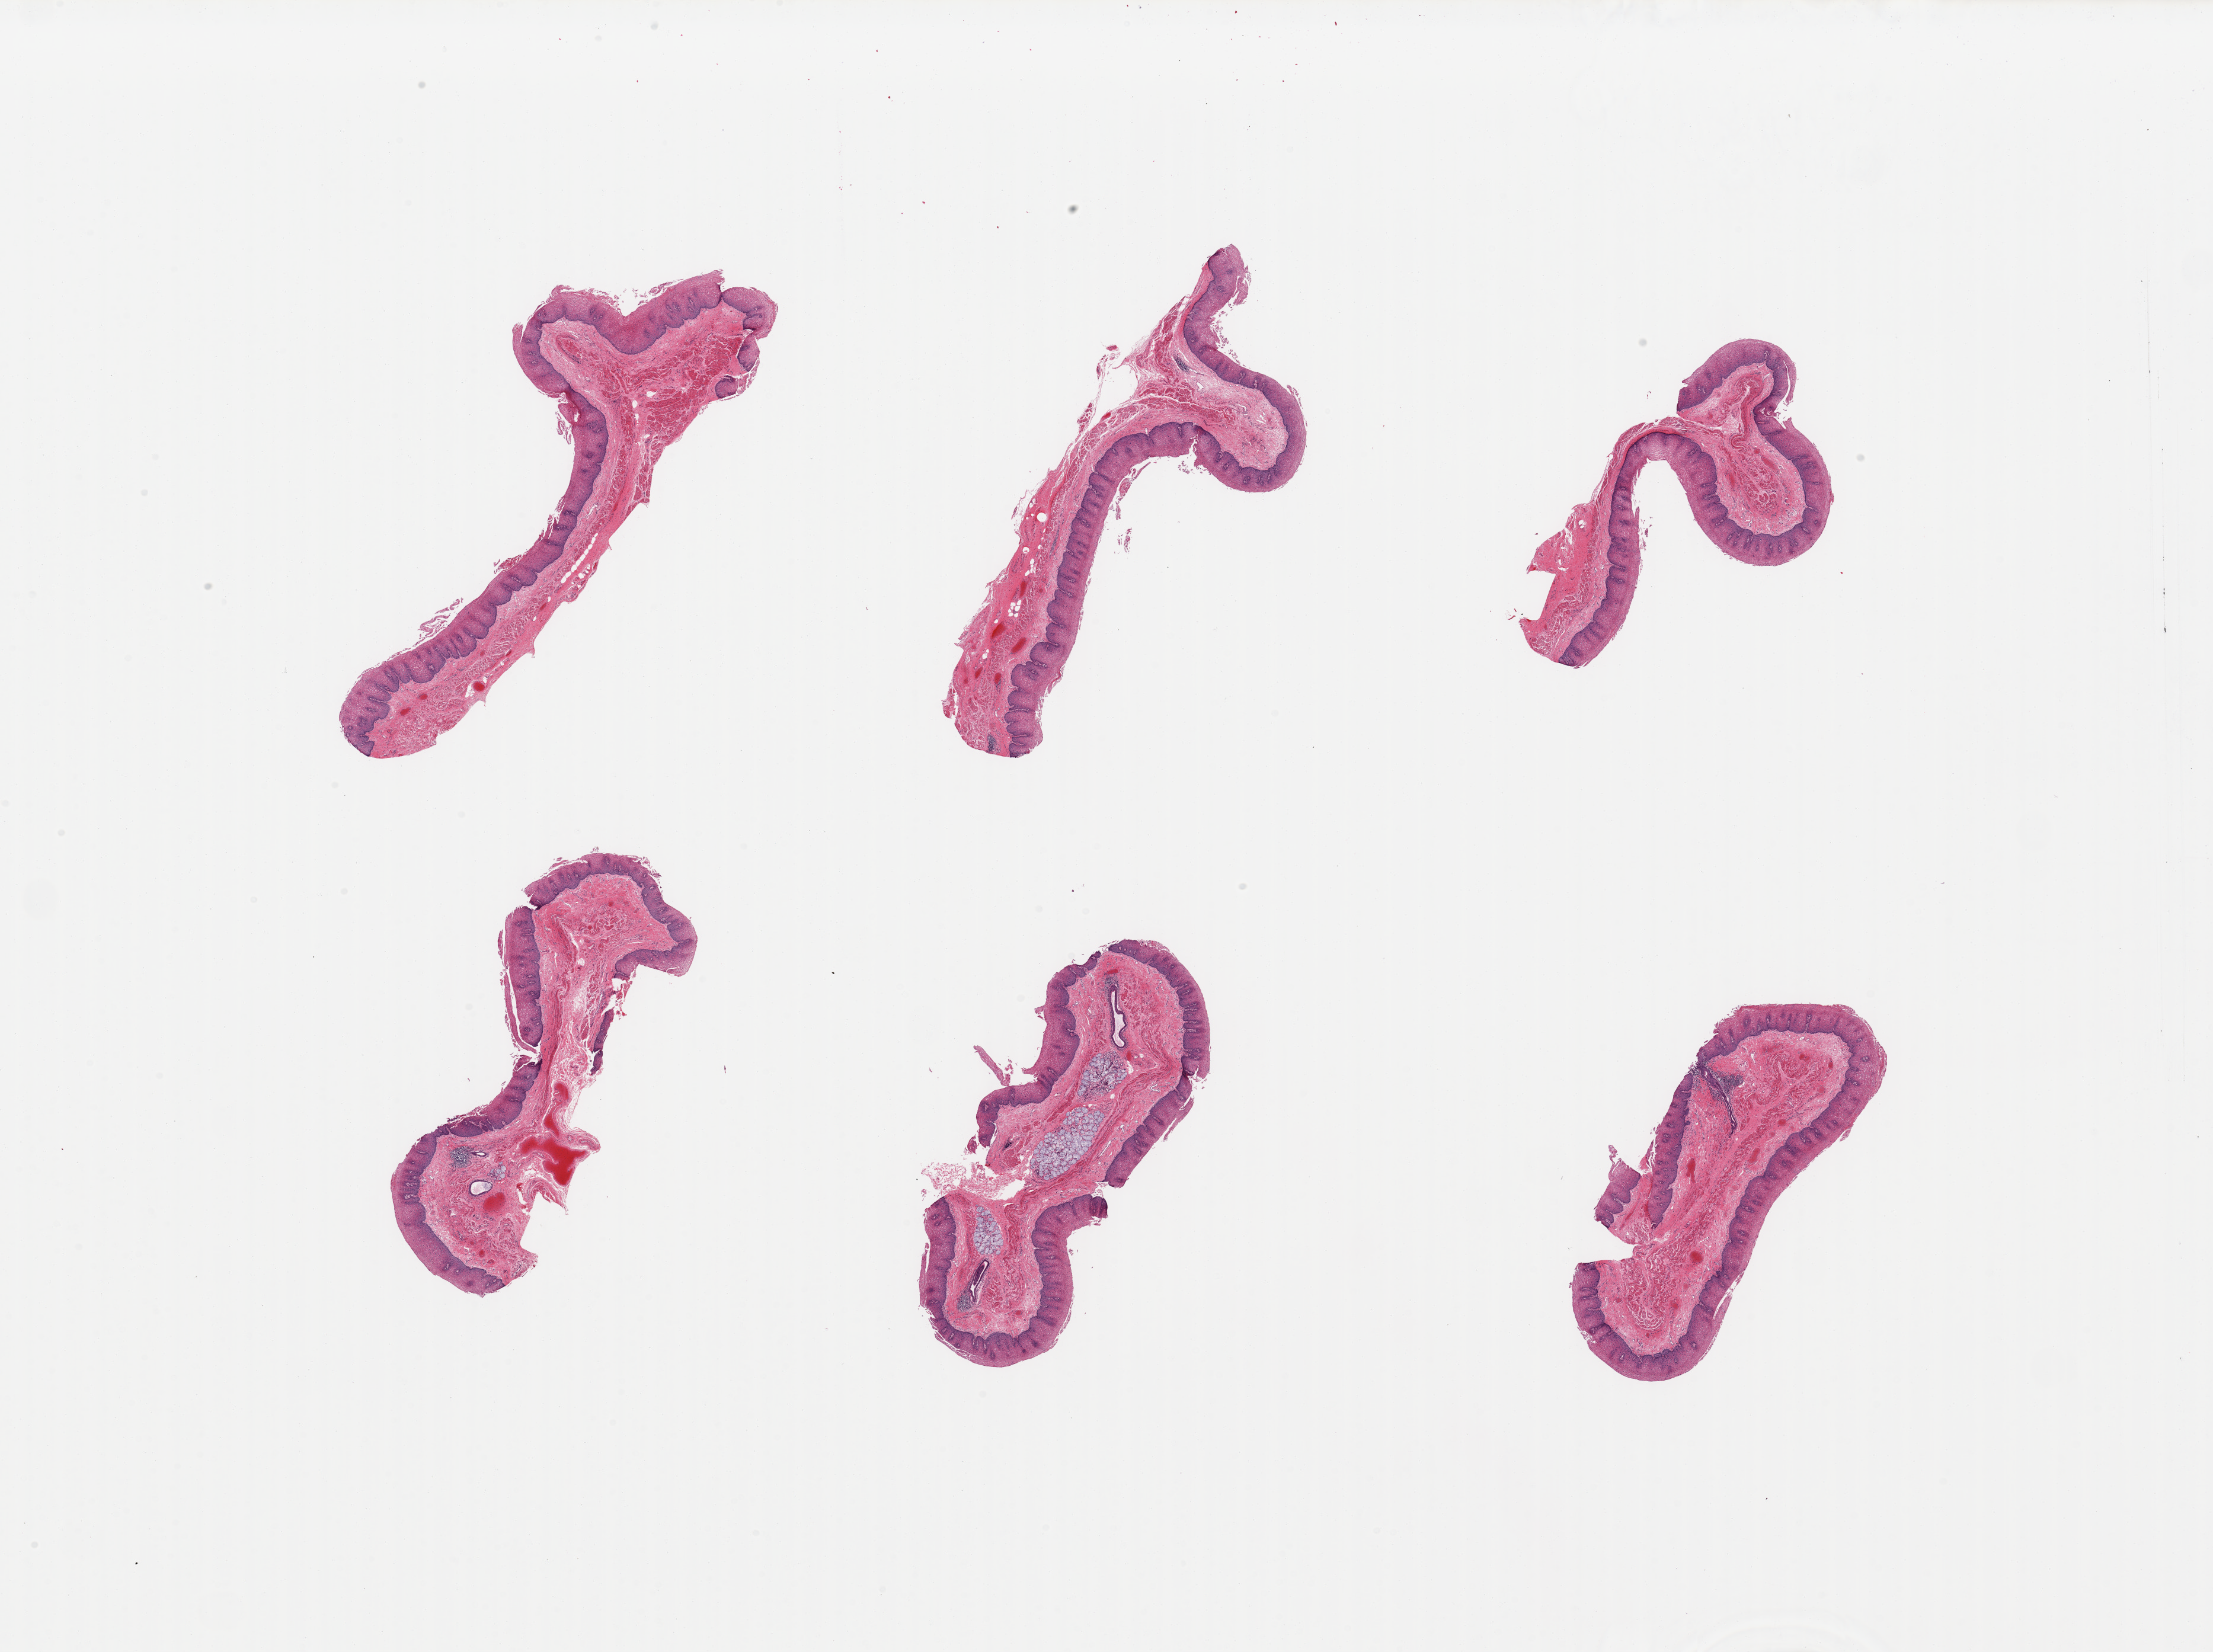
Haematoxylin and eosin whole-slide image — whole scanned area (about 29.5 x 22.1 mm, acquisition: 20x scan) shown as a low-resolution overview; PAXgene-fixed, paraffin-embedded tissue; section of esophageal mucous membrane (target tissue); donor tissue sample. Male donor.
- pathologist's review note for this sample: 6 pieces; squamous mucosa is ~0.5mm, ~50-60% thickness; A few submucosal mucus glands present